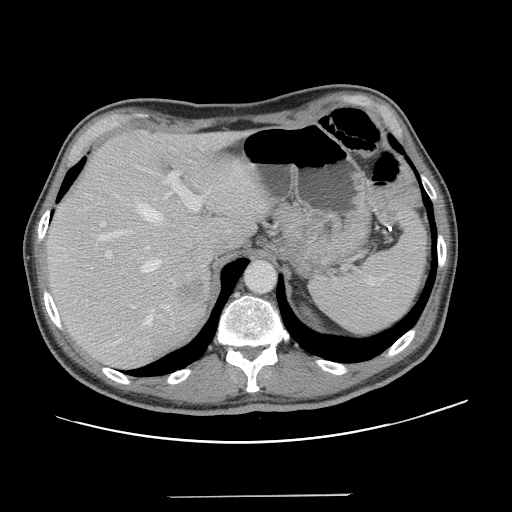
Contrast-enhanced abdominal CT, one axial slice. Slice 97 of 131 in the series (ordered by position). Intravenous contrast given. Soft-tissue window (W 400 / L 40 HU). 512 × 512 image matrix. Male patient, age 60 years. From the clinical record (not read from this slice): diagnosis: colorectal cancer liver metastases, imaged before liver resection; multiple liver metastases: no; largest metastasis: 2.5 cm; disease in both lobes: no.
Structures marked on this image (manually delineated by an expert):
- hepatic veins: bounding box <98,200,167,325> (left, top, right, bottom; pixels)
- liver: <47,132,263,368>
- planned liver remnant (the part of the liver to remain after resection): <47,132,262,353>
- portal vein (with intrahepatic branches): <99,144,211,260>
- liver metastasis: <174,277,206,307>